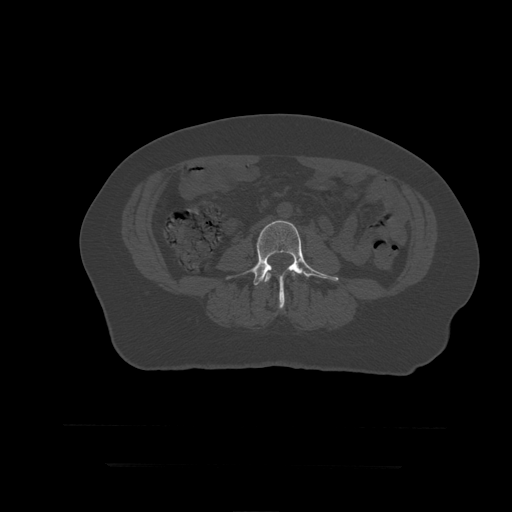
CT including the spine, one axial slice; position 103 of 399 along the scan axis; reconstruction kernel STANDARD; 120 kVp; bone window (W 1800 / L 400 HU); 1.25 mm slice thickness; 512 × 512 image matrix, field of view 450 × 450 mm. Patient age 41 years. From the clinical record (not read from this slice): primary cancer: breast.
Outlined on this slice (semi-automatically segmented with operator editing):
- L3 vertebra: bounding box [x1, y1, x2, y2] px = [265, 272, 295, 283]
- L4 vertebra: [227, 220, 339, 309]